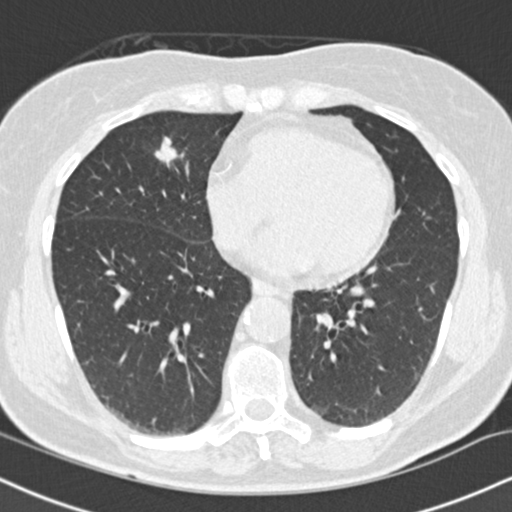
Low-dose screening chest CT, one axial slice. Slice 59 of 145 in the series (ordered by position). Reconstruction kernel B30f. Lung window (W 1500 / L -600 HU). 512 × 512 image matrix, field of view 320 × 320 mm.
Outlined on this slice (outlined manually by an expert reader):
- lesion 1 (tumor, middle lobe of right lung): bounding box <155,137,180,167> (left, top, right, bottom; pixels)